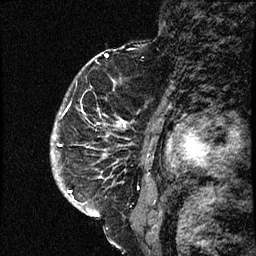
Breast MRI (dynamic contrast-enhanced), one sagittal slice. Position 52 of 66 along the scan axis. Dynamic contrast-enhanced study with each time point stored as its own series, time point 2 of 3 at this slice position (early post-contrast, ordered by acquisition time). 1.5 T. TE 4.2 ms, TR 17.6 ms. 256 × 256 image matrix, field of view 200 × 200 mm. Female patient. From the clinical record (not read from this slice): setting: breast cancer imaged before/during neoadjuvant chemotherapy; receptor status: HER2-positive.
Structures marked on this image (semi-automatically segmented with operator editing):
- analysis volume of interest (the breast-tissue region the enhancement analysis was run in; not a lesion): box from (x=52, y=69) to (x=139, y=209) px
- tumour enhancement mask (voxels above the 100 % enhancement threshold inside the analysis volume of interest): (x=53, y=121)–(x=130, y=208)